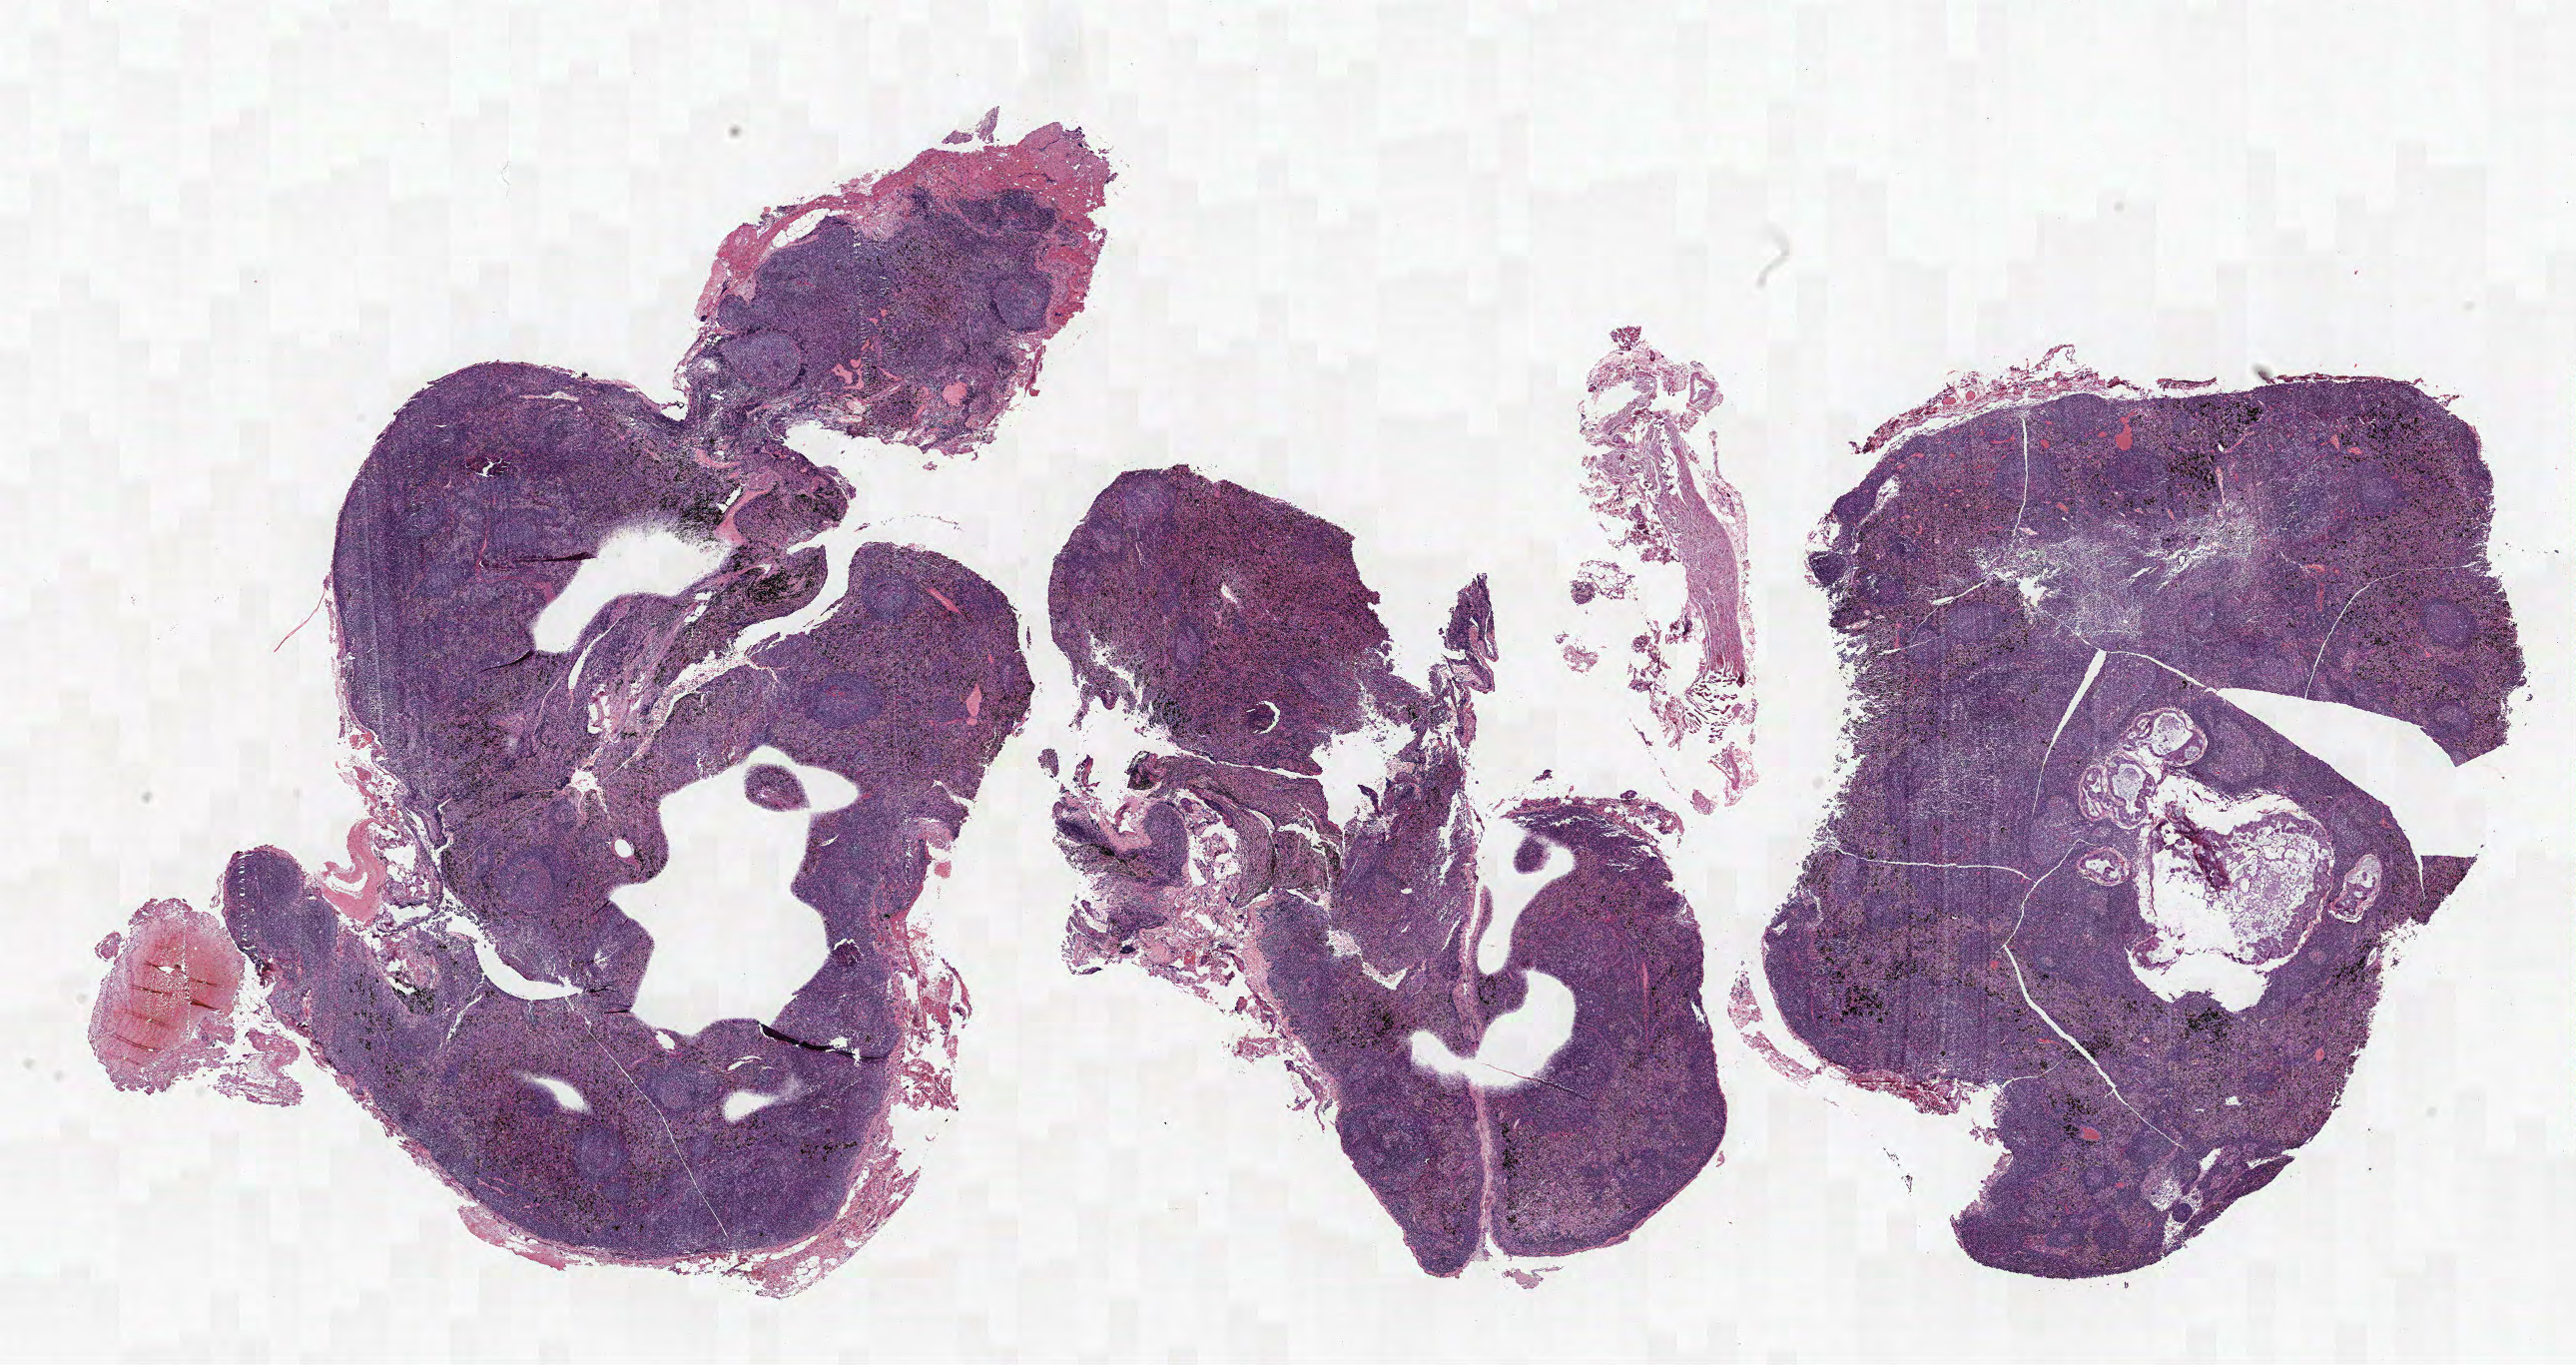
Hematoxylin and eosin (H&E) stained whole-slide image, whole scanned area (about 20.6 x 10.9 mm, slide scanned at 40x) shown as a low-resolution overview. FFPE section. Lung. Female, age 66 at enrolment. Current smoker at enrolment. Grade: moderately differentiated (G2).
* tumour size (pathology): 11 mm
* stage (AJCC 6th edition): IIA
* participant's lung-cancer diagnosis: Adenocarcinoma, NOS
* primary tumour location (clinical record): right lower lobe
* ICD-O-3 topography: lower lobe of lung (C34.3)